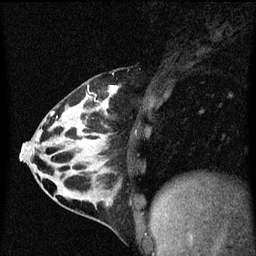
Breast MRI (dynamic contrast-enhanced), one sagittal slice; slice 25 of 60 in the series (ordered by position); dynamic contrast-enhanced series, image 2 of 3 at this slice position (ordered by acquisition); 1.5 T; TE 4.2 ms, TR 8.4 ms; 2 mm slice thickness; 256 × 256 image matrix, field of view 200 × 200 mm. Patient: female, 32 years.
Outlined on this slice (semi-automatic segmentation, software-assisted and operator-edited):
- analysis volume of interest (the breast-tissue region the enhancement analysis was run in; not a lesion): bounding box (x1, y1, x2, y2) in pixels: (34, 74, 151, 169)
- tumour enhancement mask (voxels above the 70 % enhancement threshold inside the analysis volume of interest): (52, 86, 120, 115)